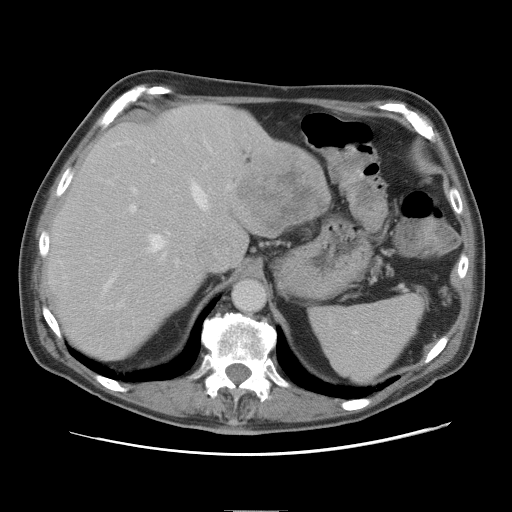
Contrast-enhanced abdominal CT, one axial slice. Position 58 of 89 along the scan axis. 120 kVp. Intravenous contrast given. Soft-tissue window (W 400 / L 40 HU). 5 mm slice thickness. 512 × 512 image matrix, field of view 375 × 375 mm. Male patient, age 69 years. Case-level facts recorded for this patient, not image findings: diagnosis: colorectal cancer liver metastases, imaged before liver resection; multiple liver metastases: no; largest metastasis: 8.5 cm; disease in both lobes: no.
Outlined on this slice (manually delineated by an expert):
- hepatic veins: box from (x=105, y=178) to (x=210, y=290) px
- liver: (x=48, y=104)–(x=329, y=359)
- planned liver remnant (the part of the liver to remain after resection): (x=48, y=104)–(x=245, y=359)
- portal vein (with intrahepatic branches): (x=120, y=141)–(x=230, y=304)
- liver metastasis: (x=235, y=170)–(x=329, y=234)